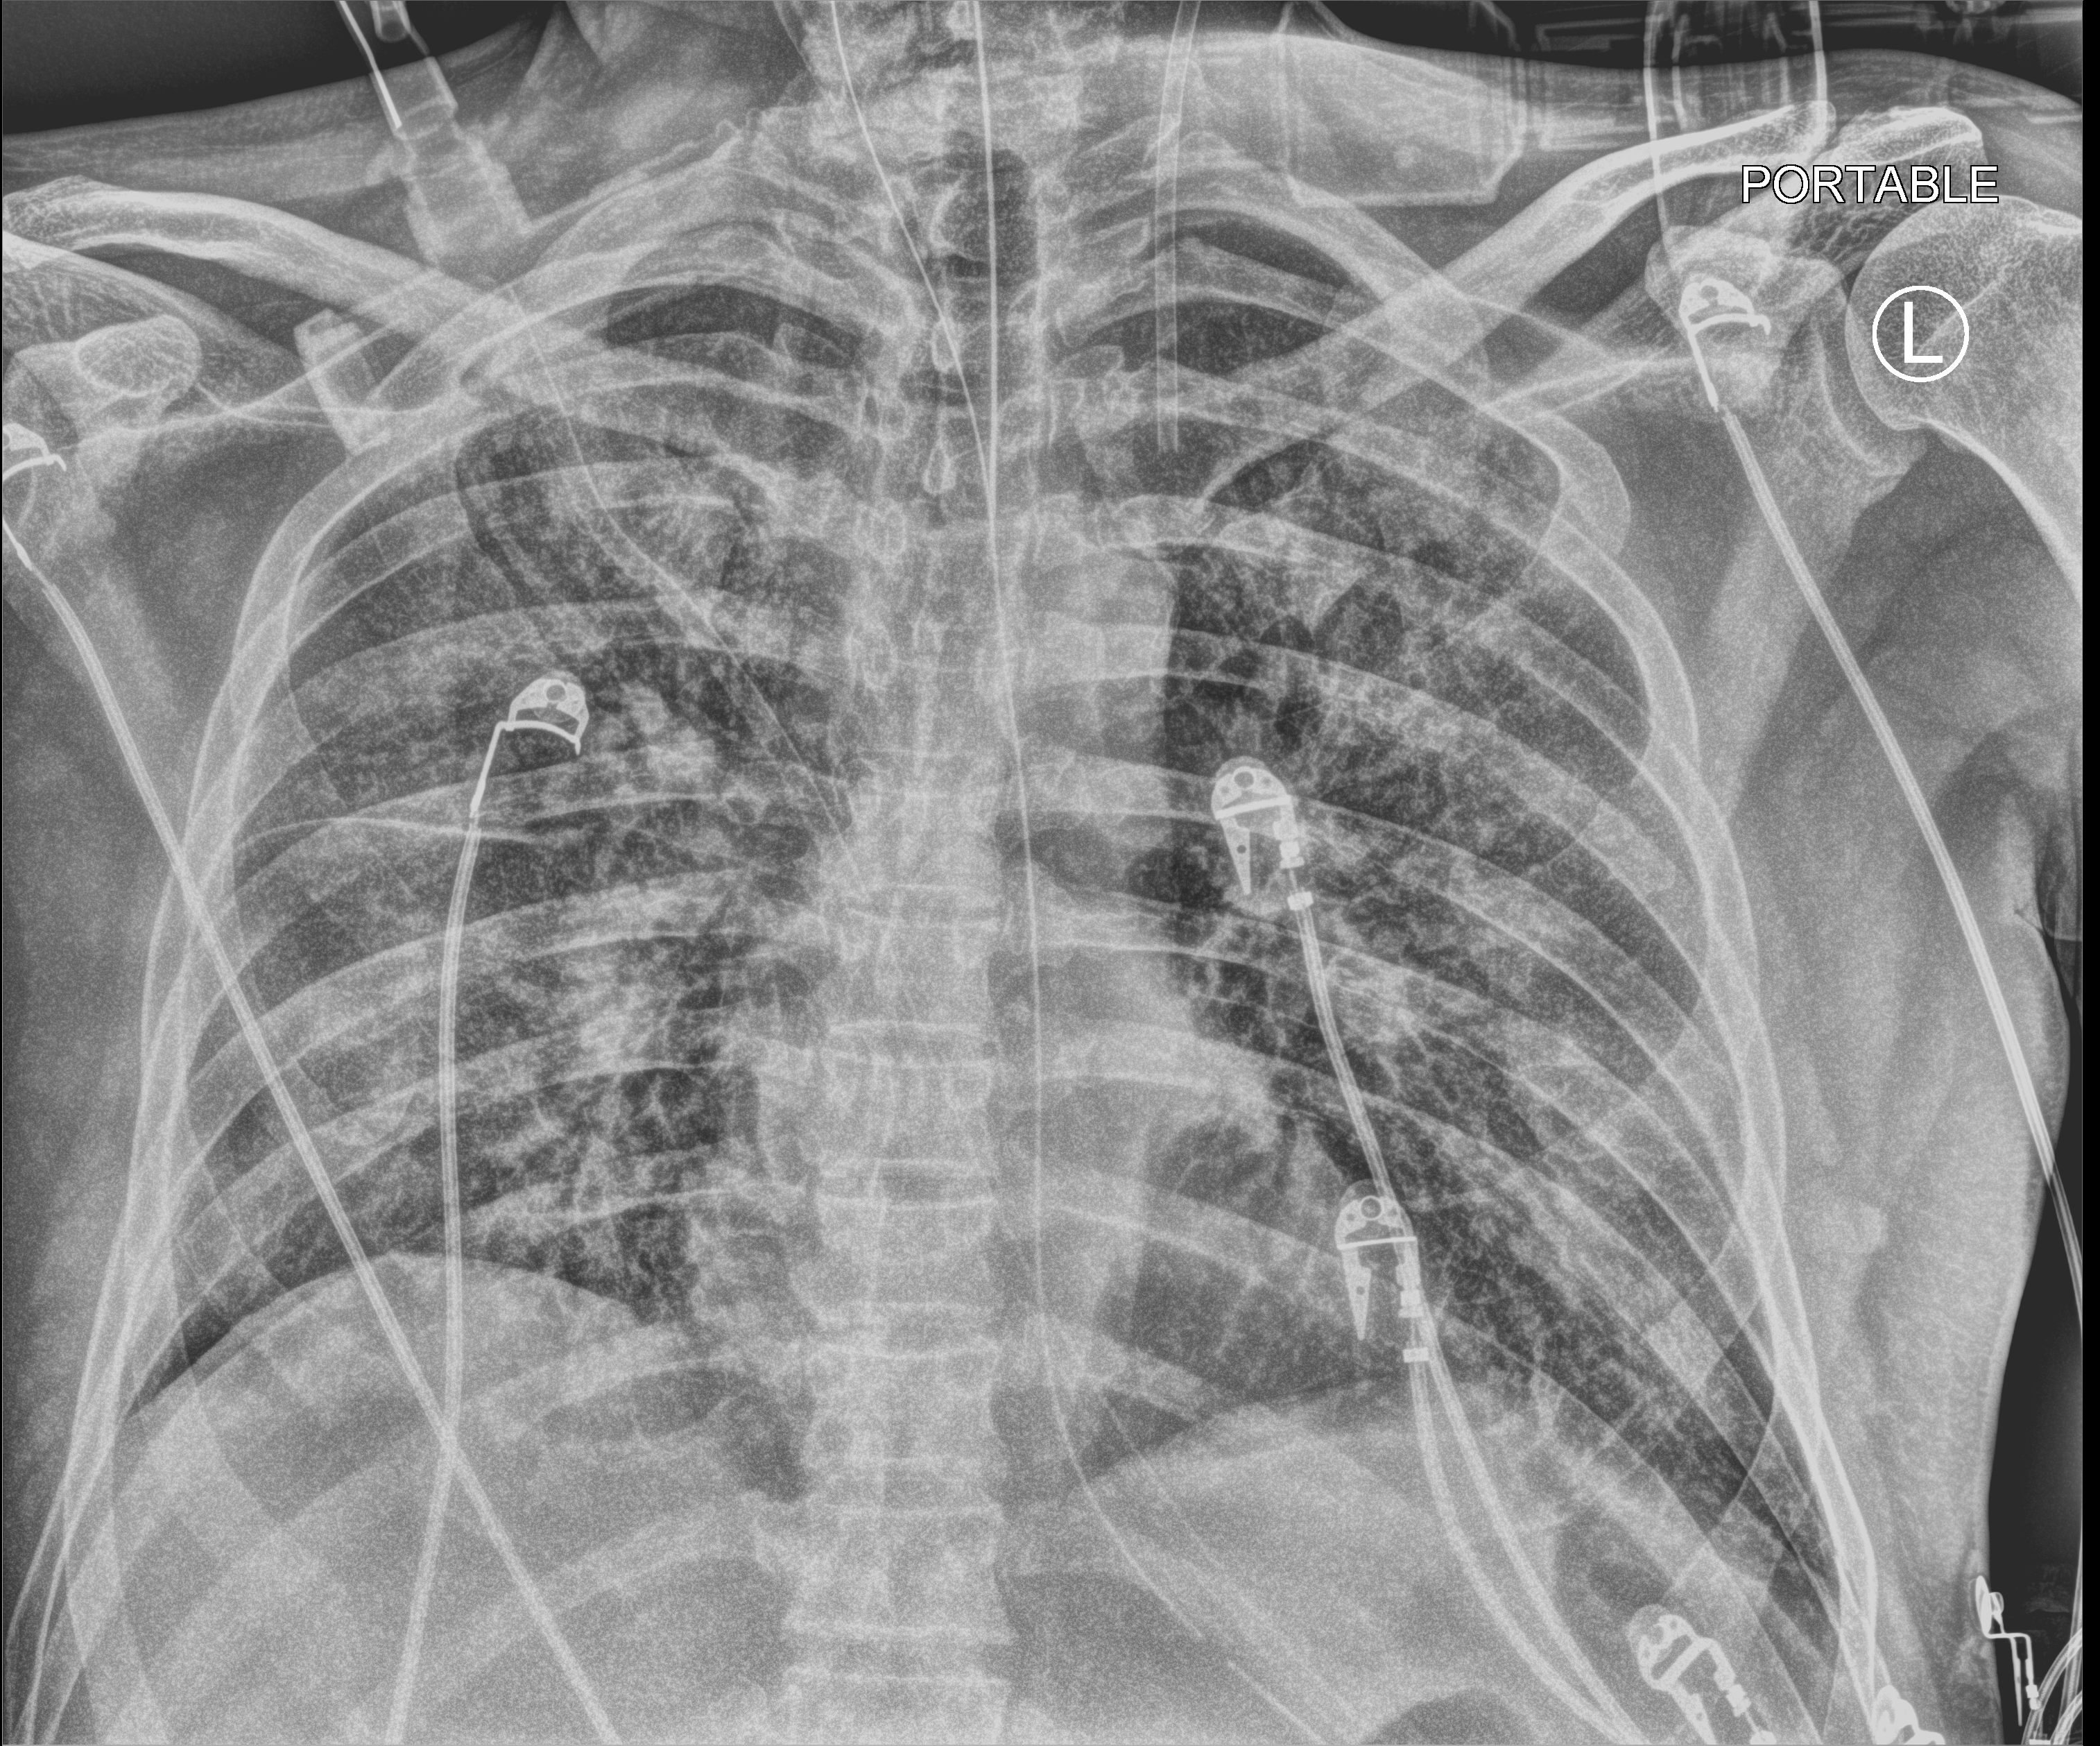
Bedside chest radiograph (computed radiography); anteroposterior (AP) projection. Male patient hospitalised with COVID-19, age 60–74 years.
Admission-level facts for this patient (not findings on this image; timing relative to this image not recorded):
- mechanically ventilated during this hospital stay: yes
- admitted to intensive care during this hospital stay: yes
- length of hospital stay: 8 days